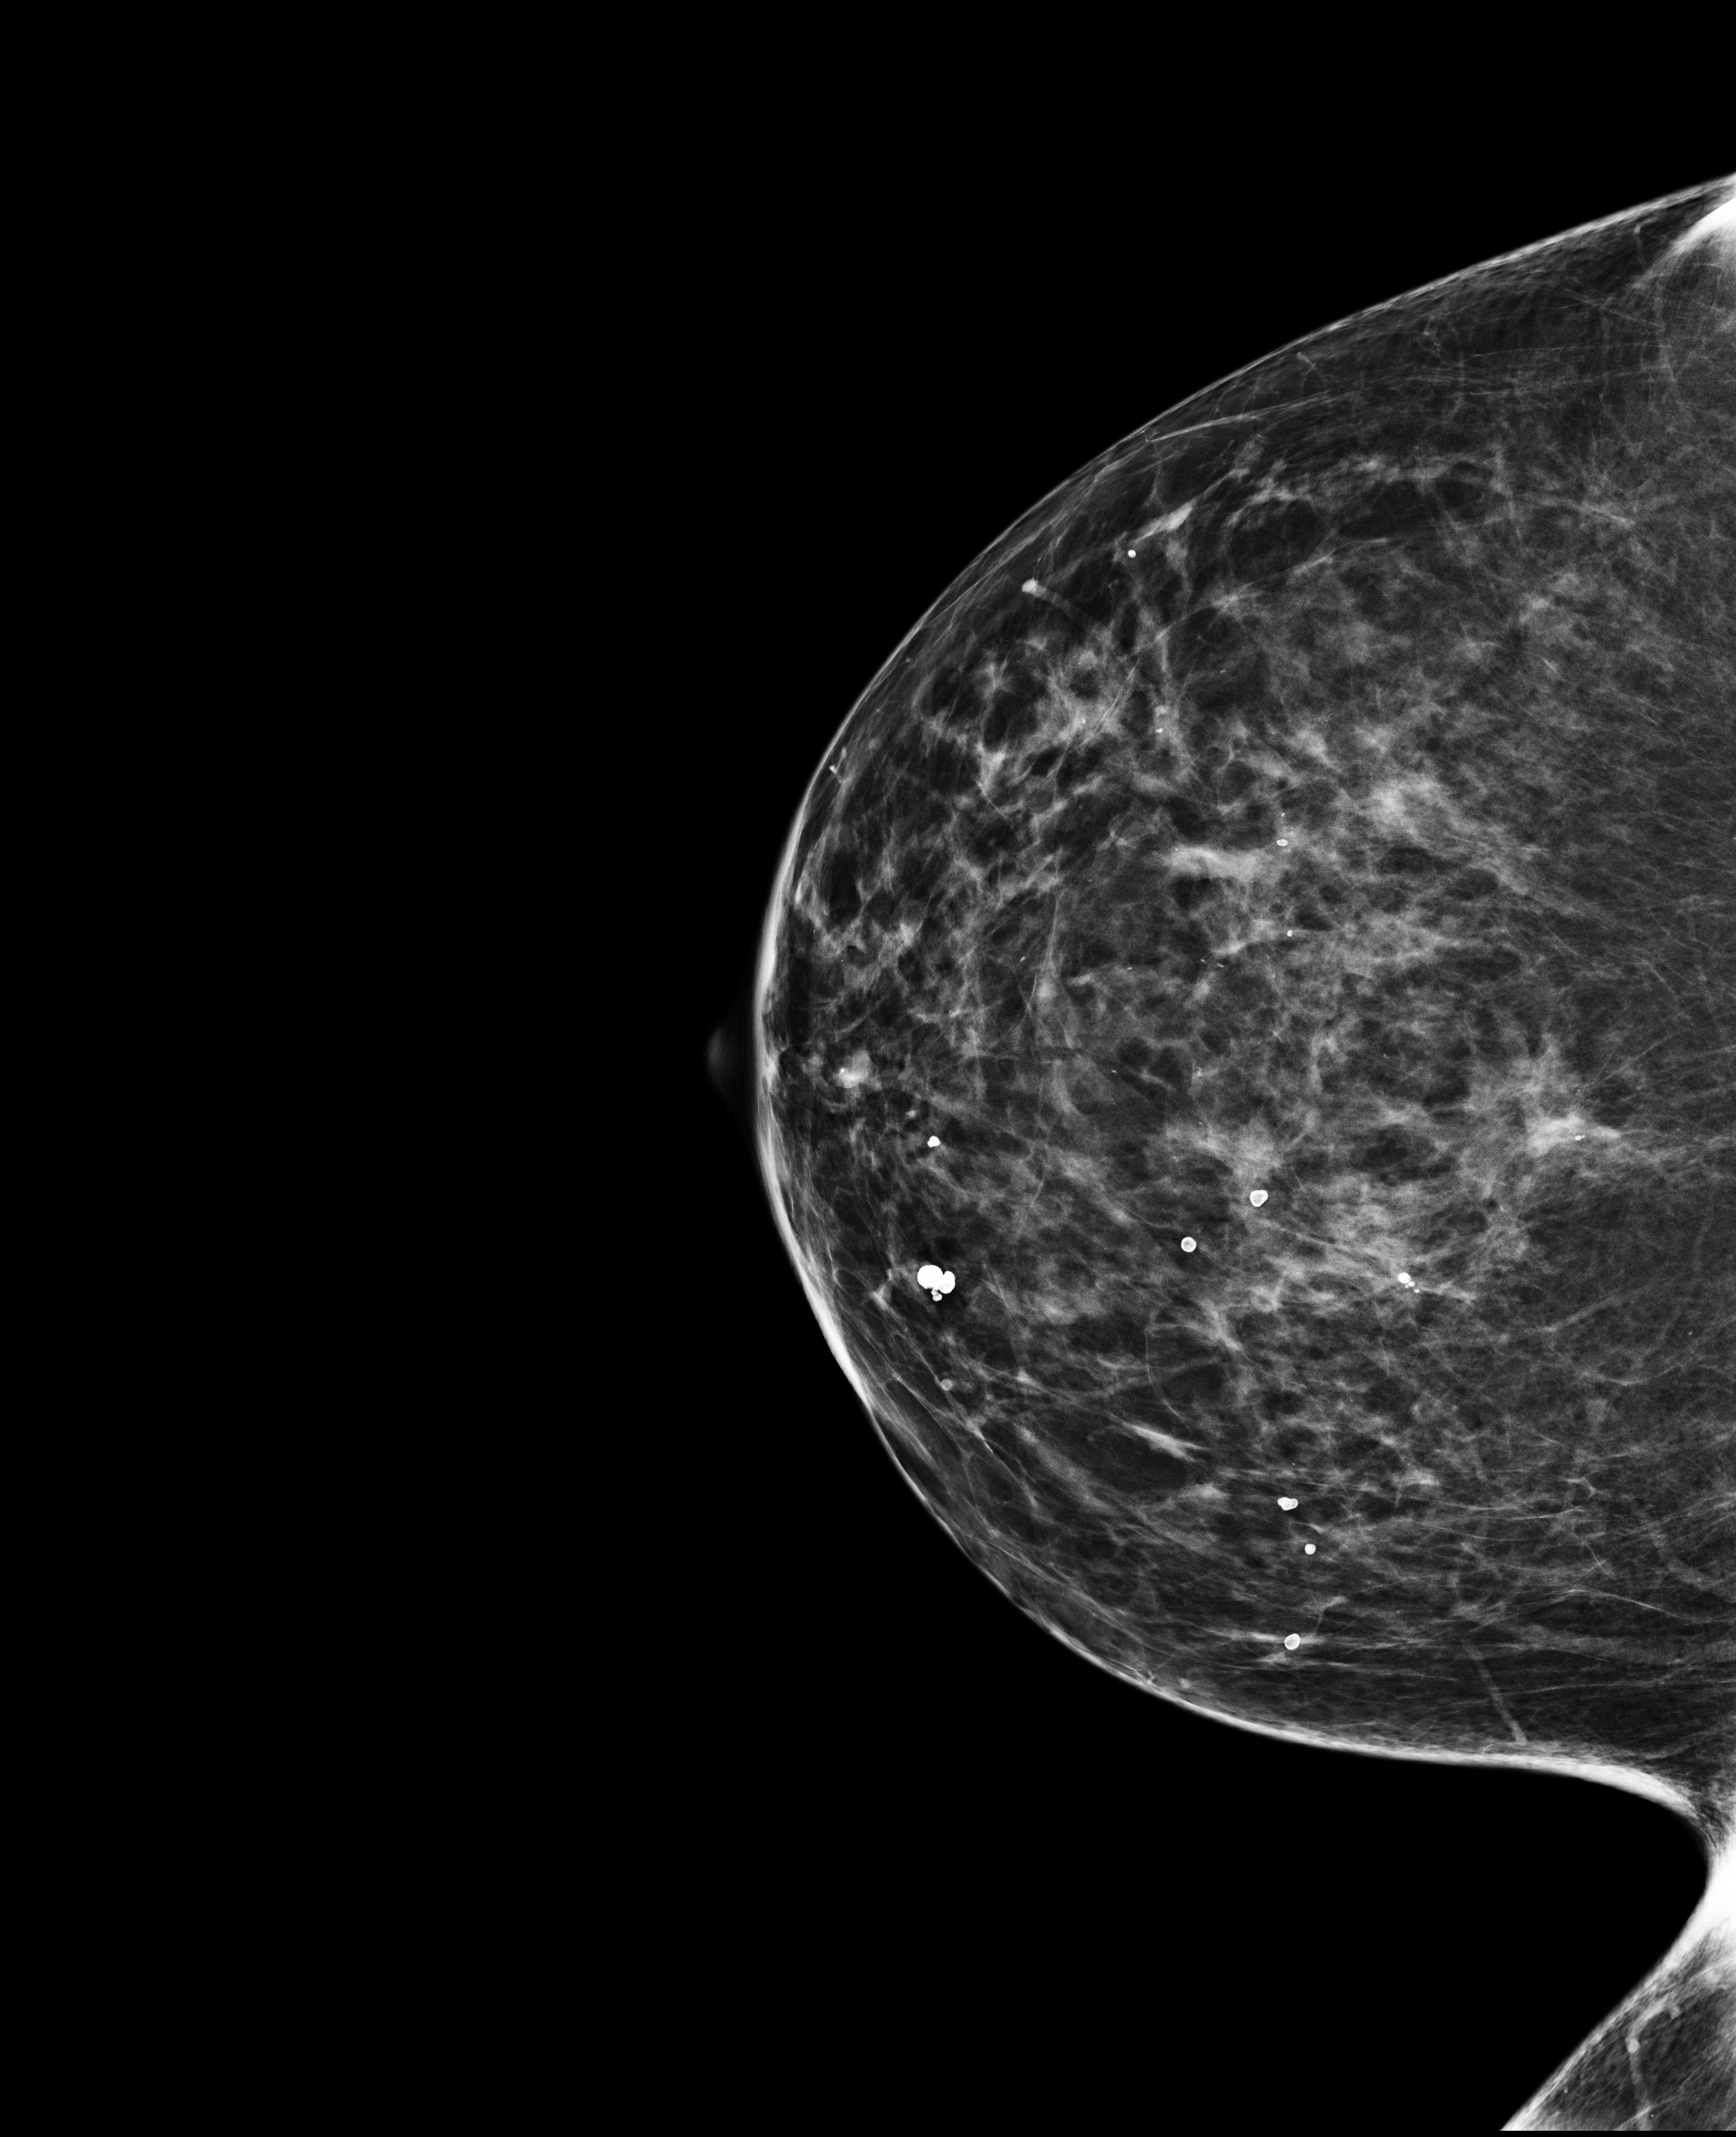
Full-field digital mammogram (FFDM), right breast, cranio-caudal projection, annual screening mammography examination, compressed breast thickness 68 mm, system: Selenia Dimensions. Patient aged 65 years (female).
- BI-RADS breast density category at the screening exam (both breasts, scale 1–4): 3
- final BI-RADS category for the screening round (tomosynthesis exam, both breasts): category 2
- recall: no recall after this screen